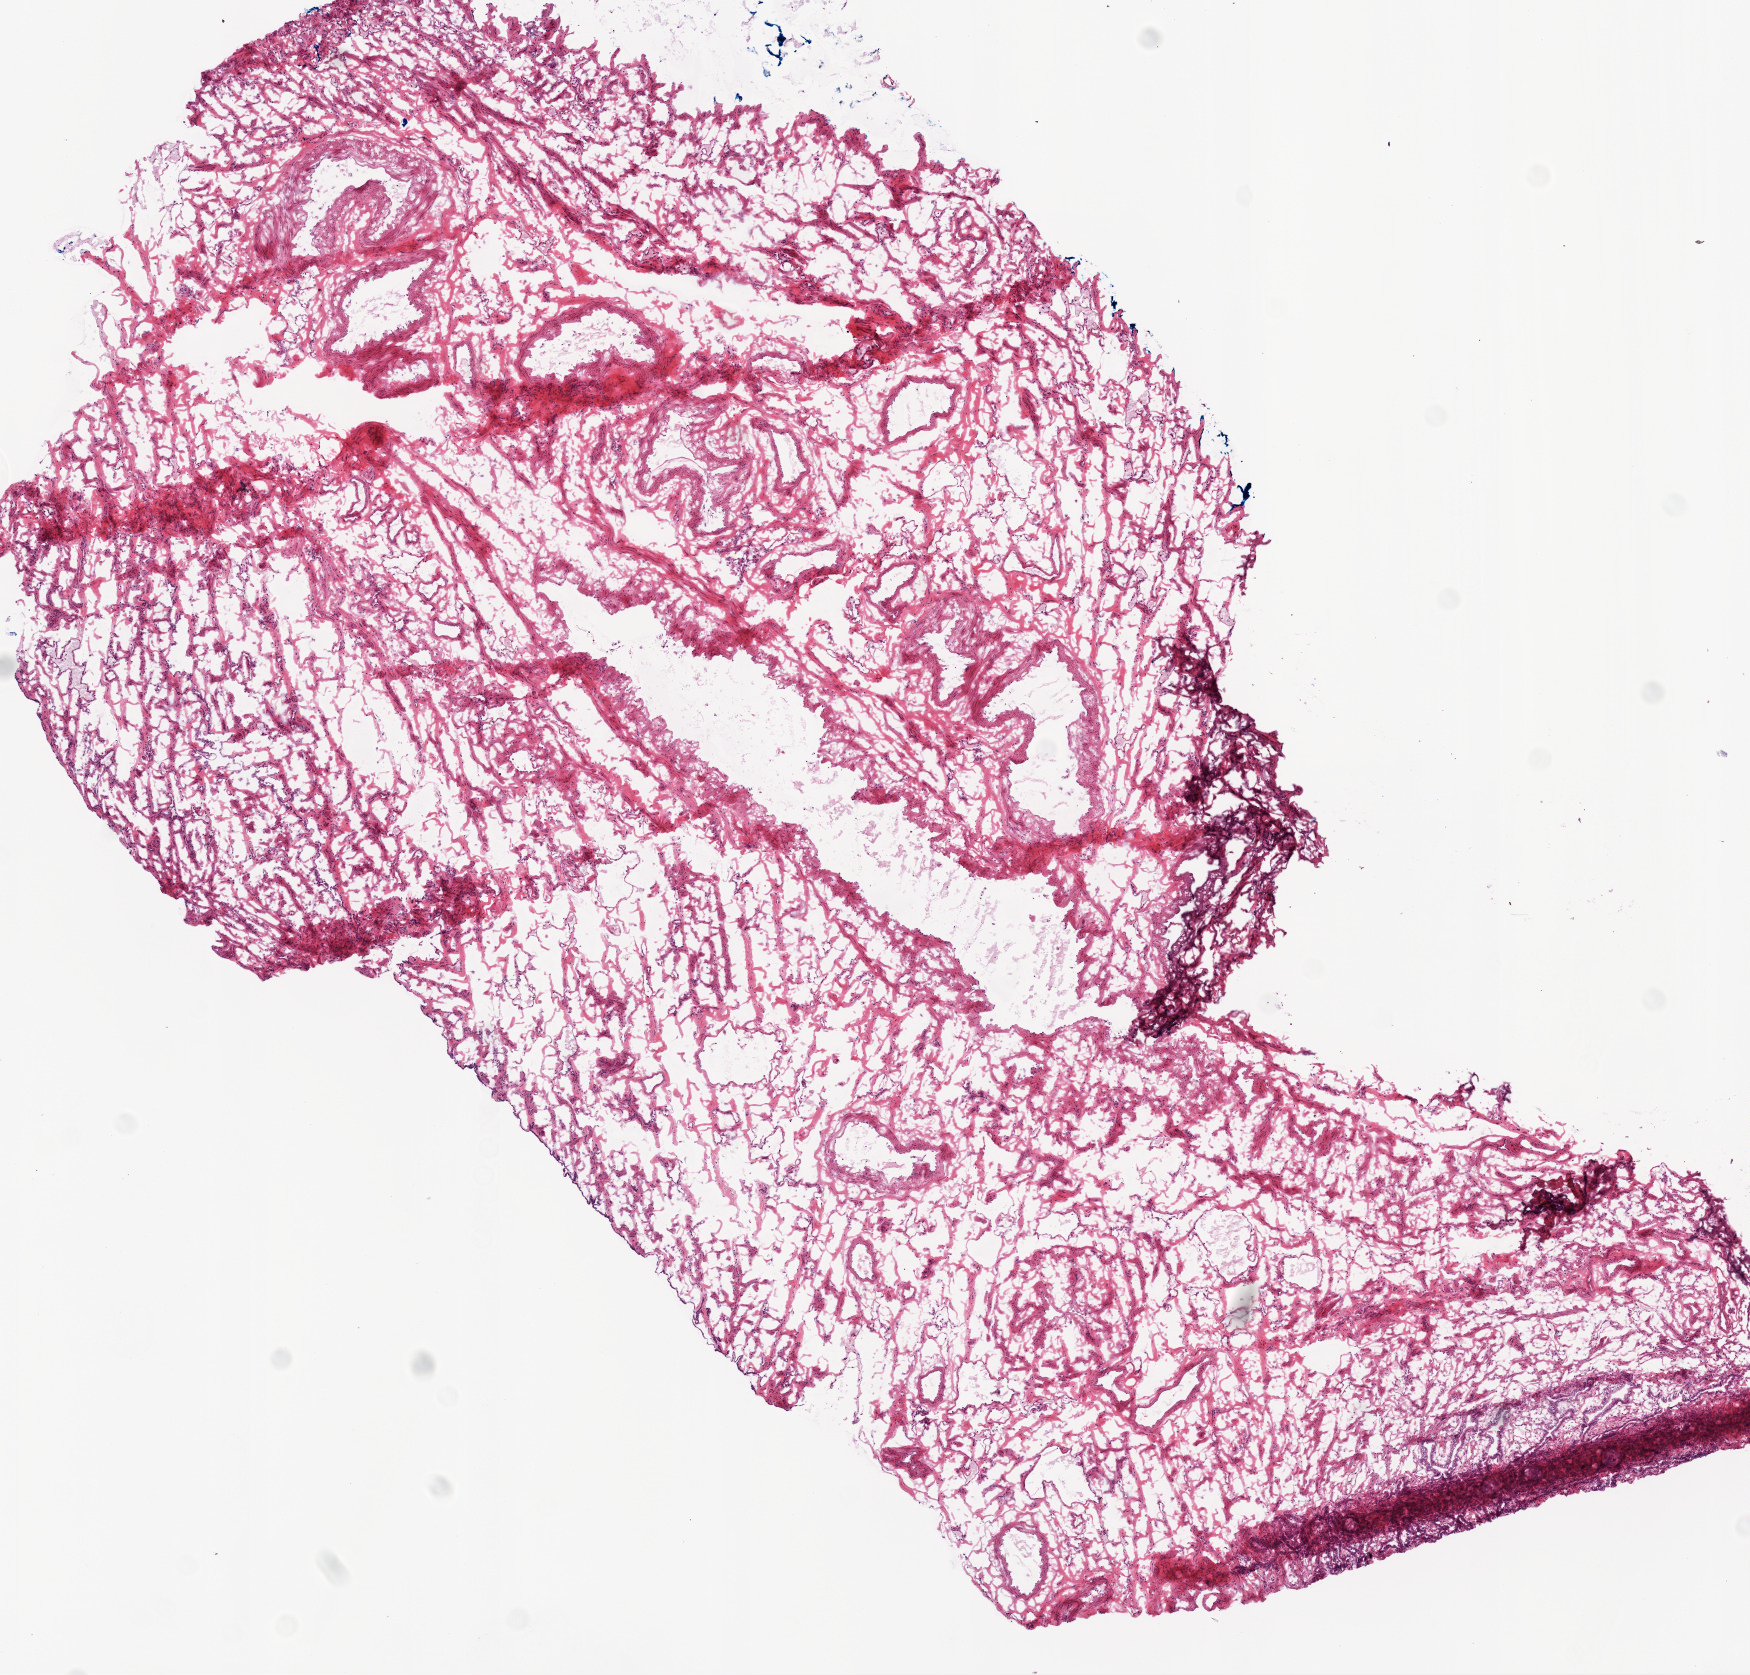
Whole-slide histology image, Hematoxylin and eosin (H&E) stained, shown as a low-resolution overview of the whole scanned area (about 7.0 x 6.7 mm, from a 20x scan). Frozen section from the top of the tissue portion. Sample: solid tissue normal (non-tumour tissue), ovary. Patient: female, age at initial diagnosis 47 years.
This section: solid tissue normal (non-tumour) sample from the same patient. Patient diagnosis: Serous cystadenocarcinoma, NOS.